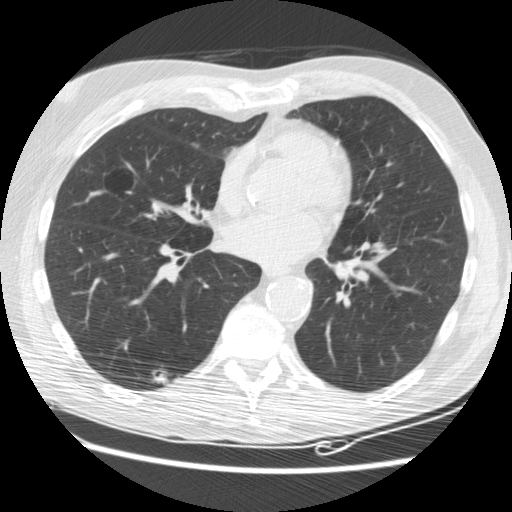
Low-dose screening chest CT, one axial slice. Slice 80 of 176 in the series (ordered by position). Reconstruction kernel STANDARD. 120 kVp. Lung window (W 1500 / L -600 HU). 2.5 mm slice thickness. 512 × 512 image matrix, field of view 347 × 347 mm.
Outlined on this slice (outlined manually by an expert reader):
- lesion 2 (tumor, lower lobe of right lung): bounding box [x1, y1, x2, y2] px = [153, 368, 172, 384]